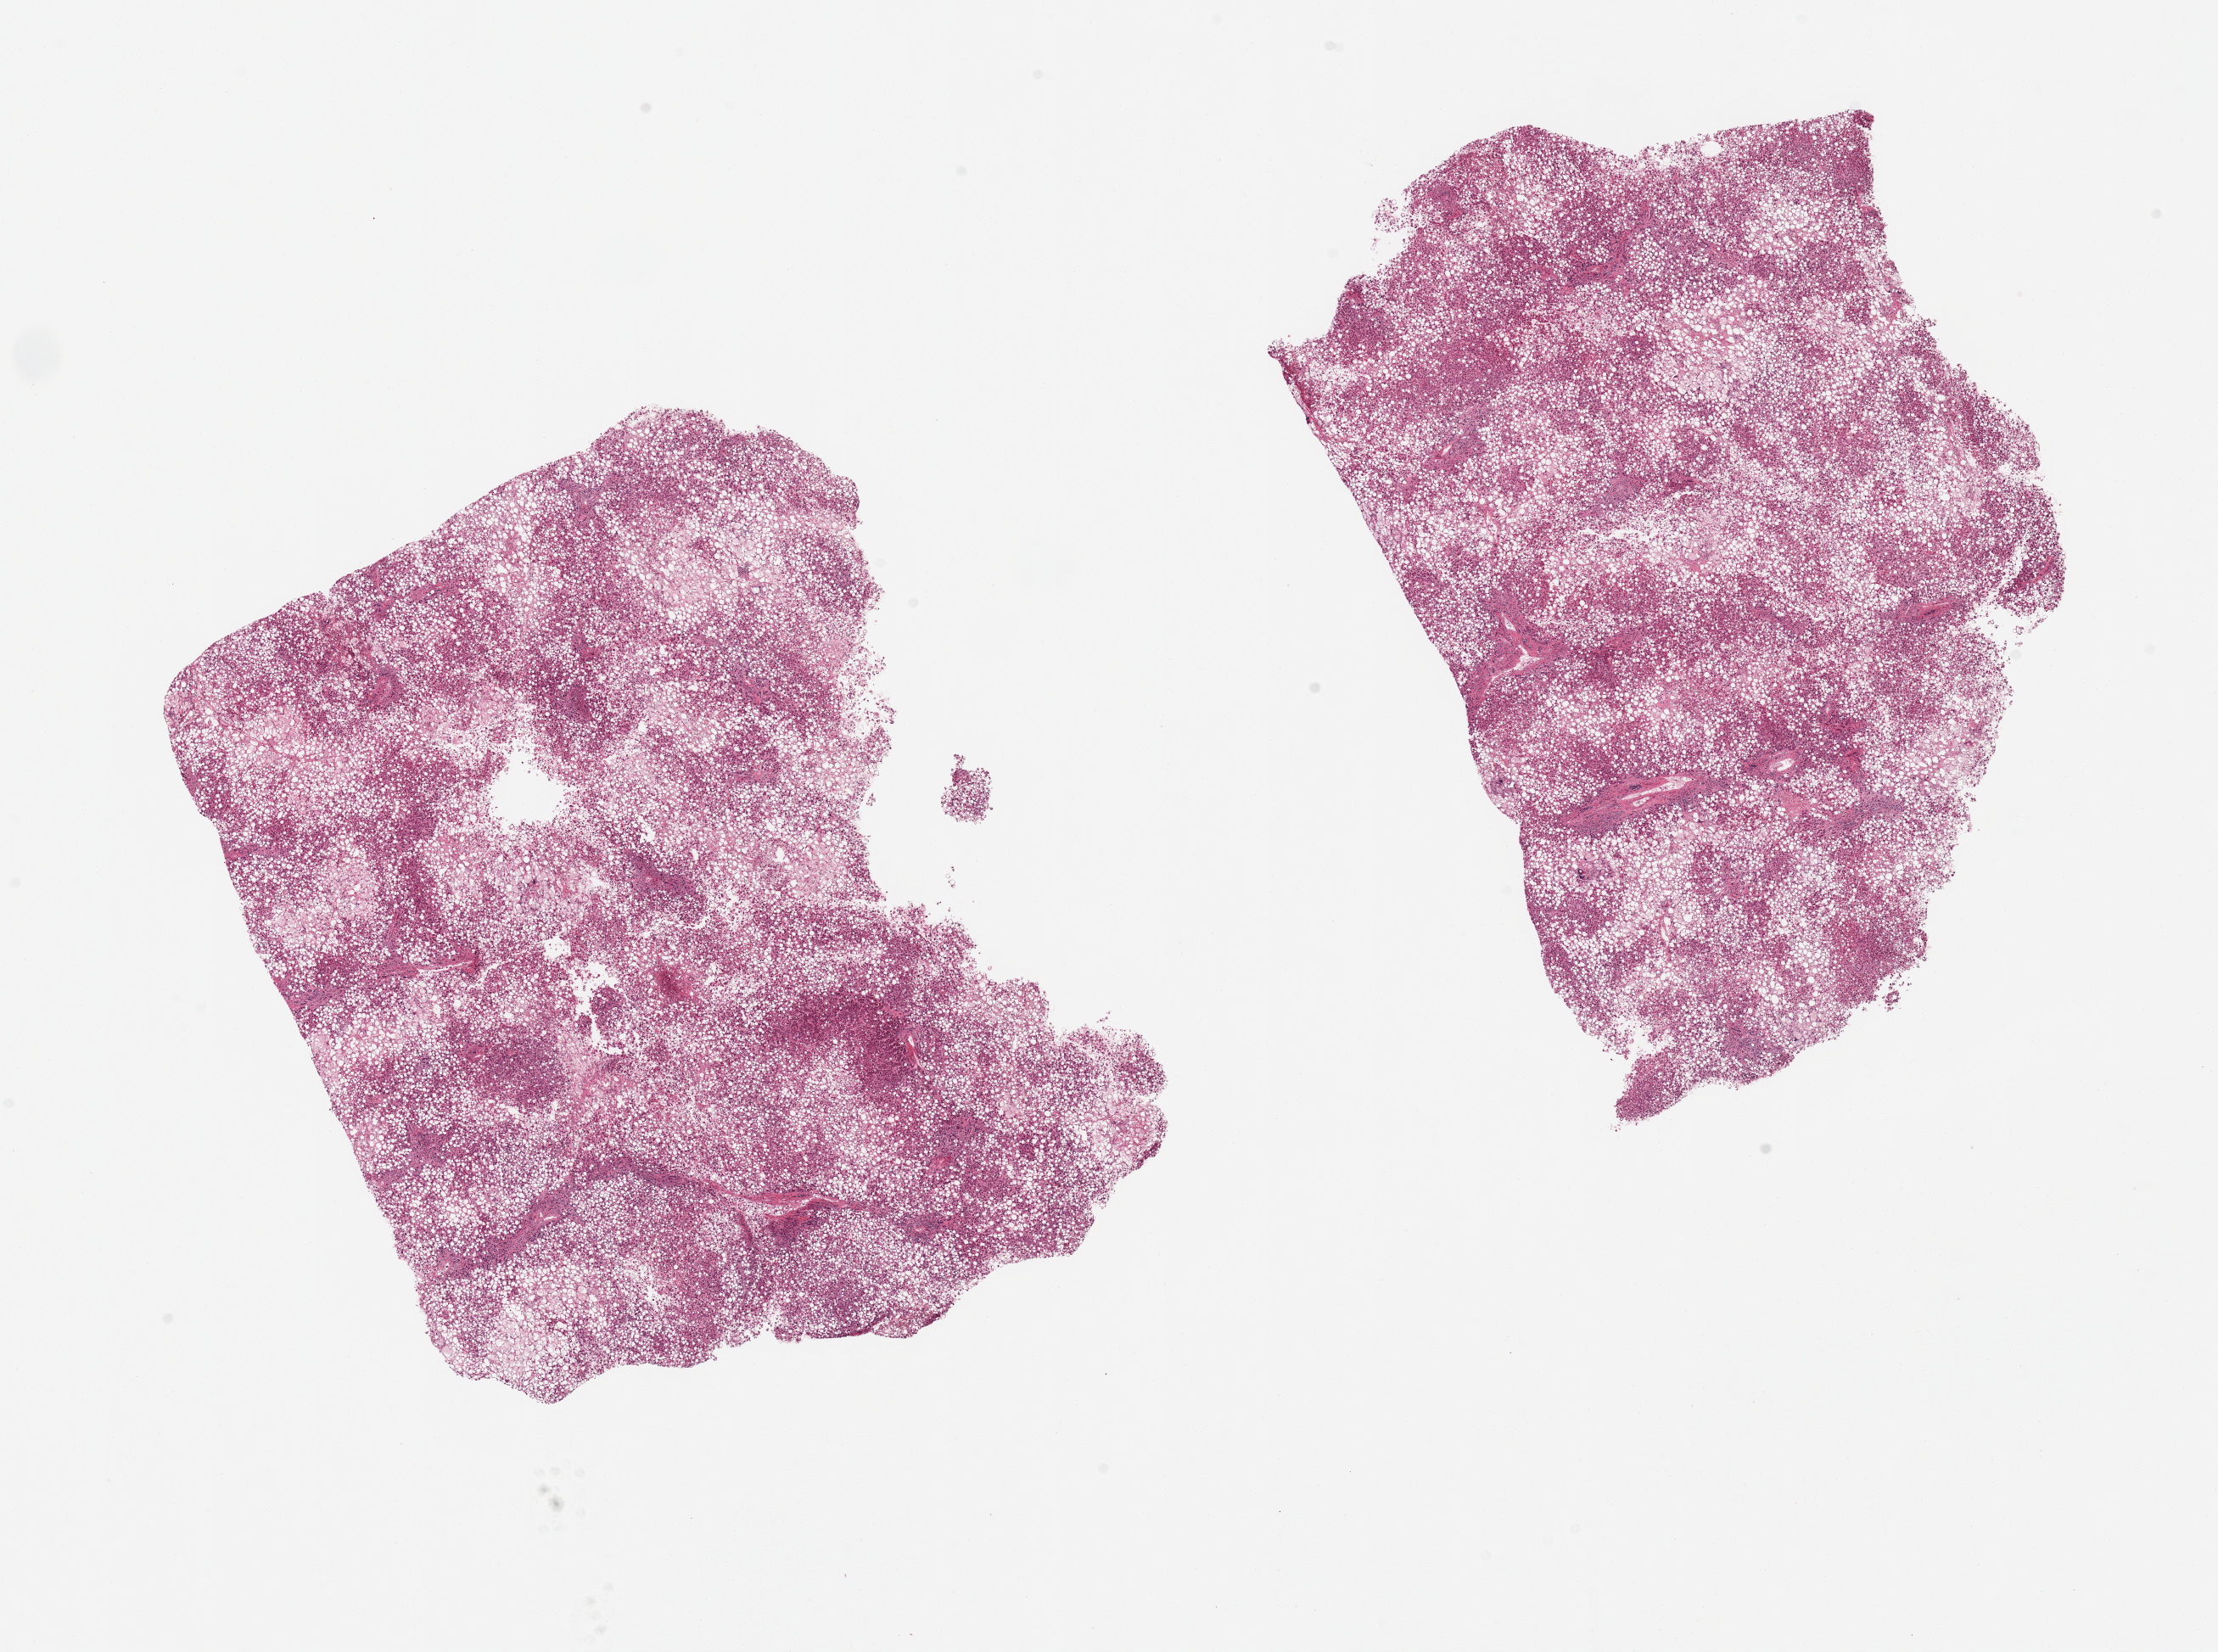
Whole-slide image, hematoxylin and eosin (H&E) stain, whole scanned area (about 20.7 x 15.4 mm, from a 20x scan) shown as a low-resolution overview; PAXgene-fixed, paraffin-embedded tissue; target tissue: liver; donor tissue sample. Male donor.
- reviewer comment on this tissue sample: 2 pieces marked macrovesicular steatosis involves >90% of parenchyma